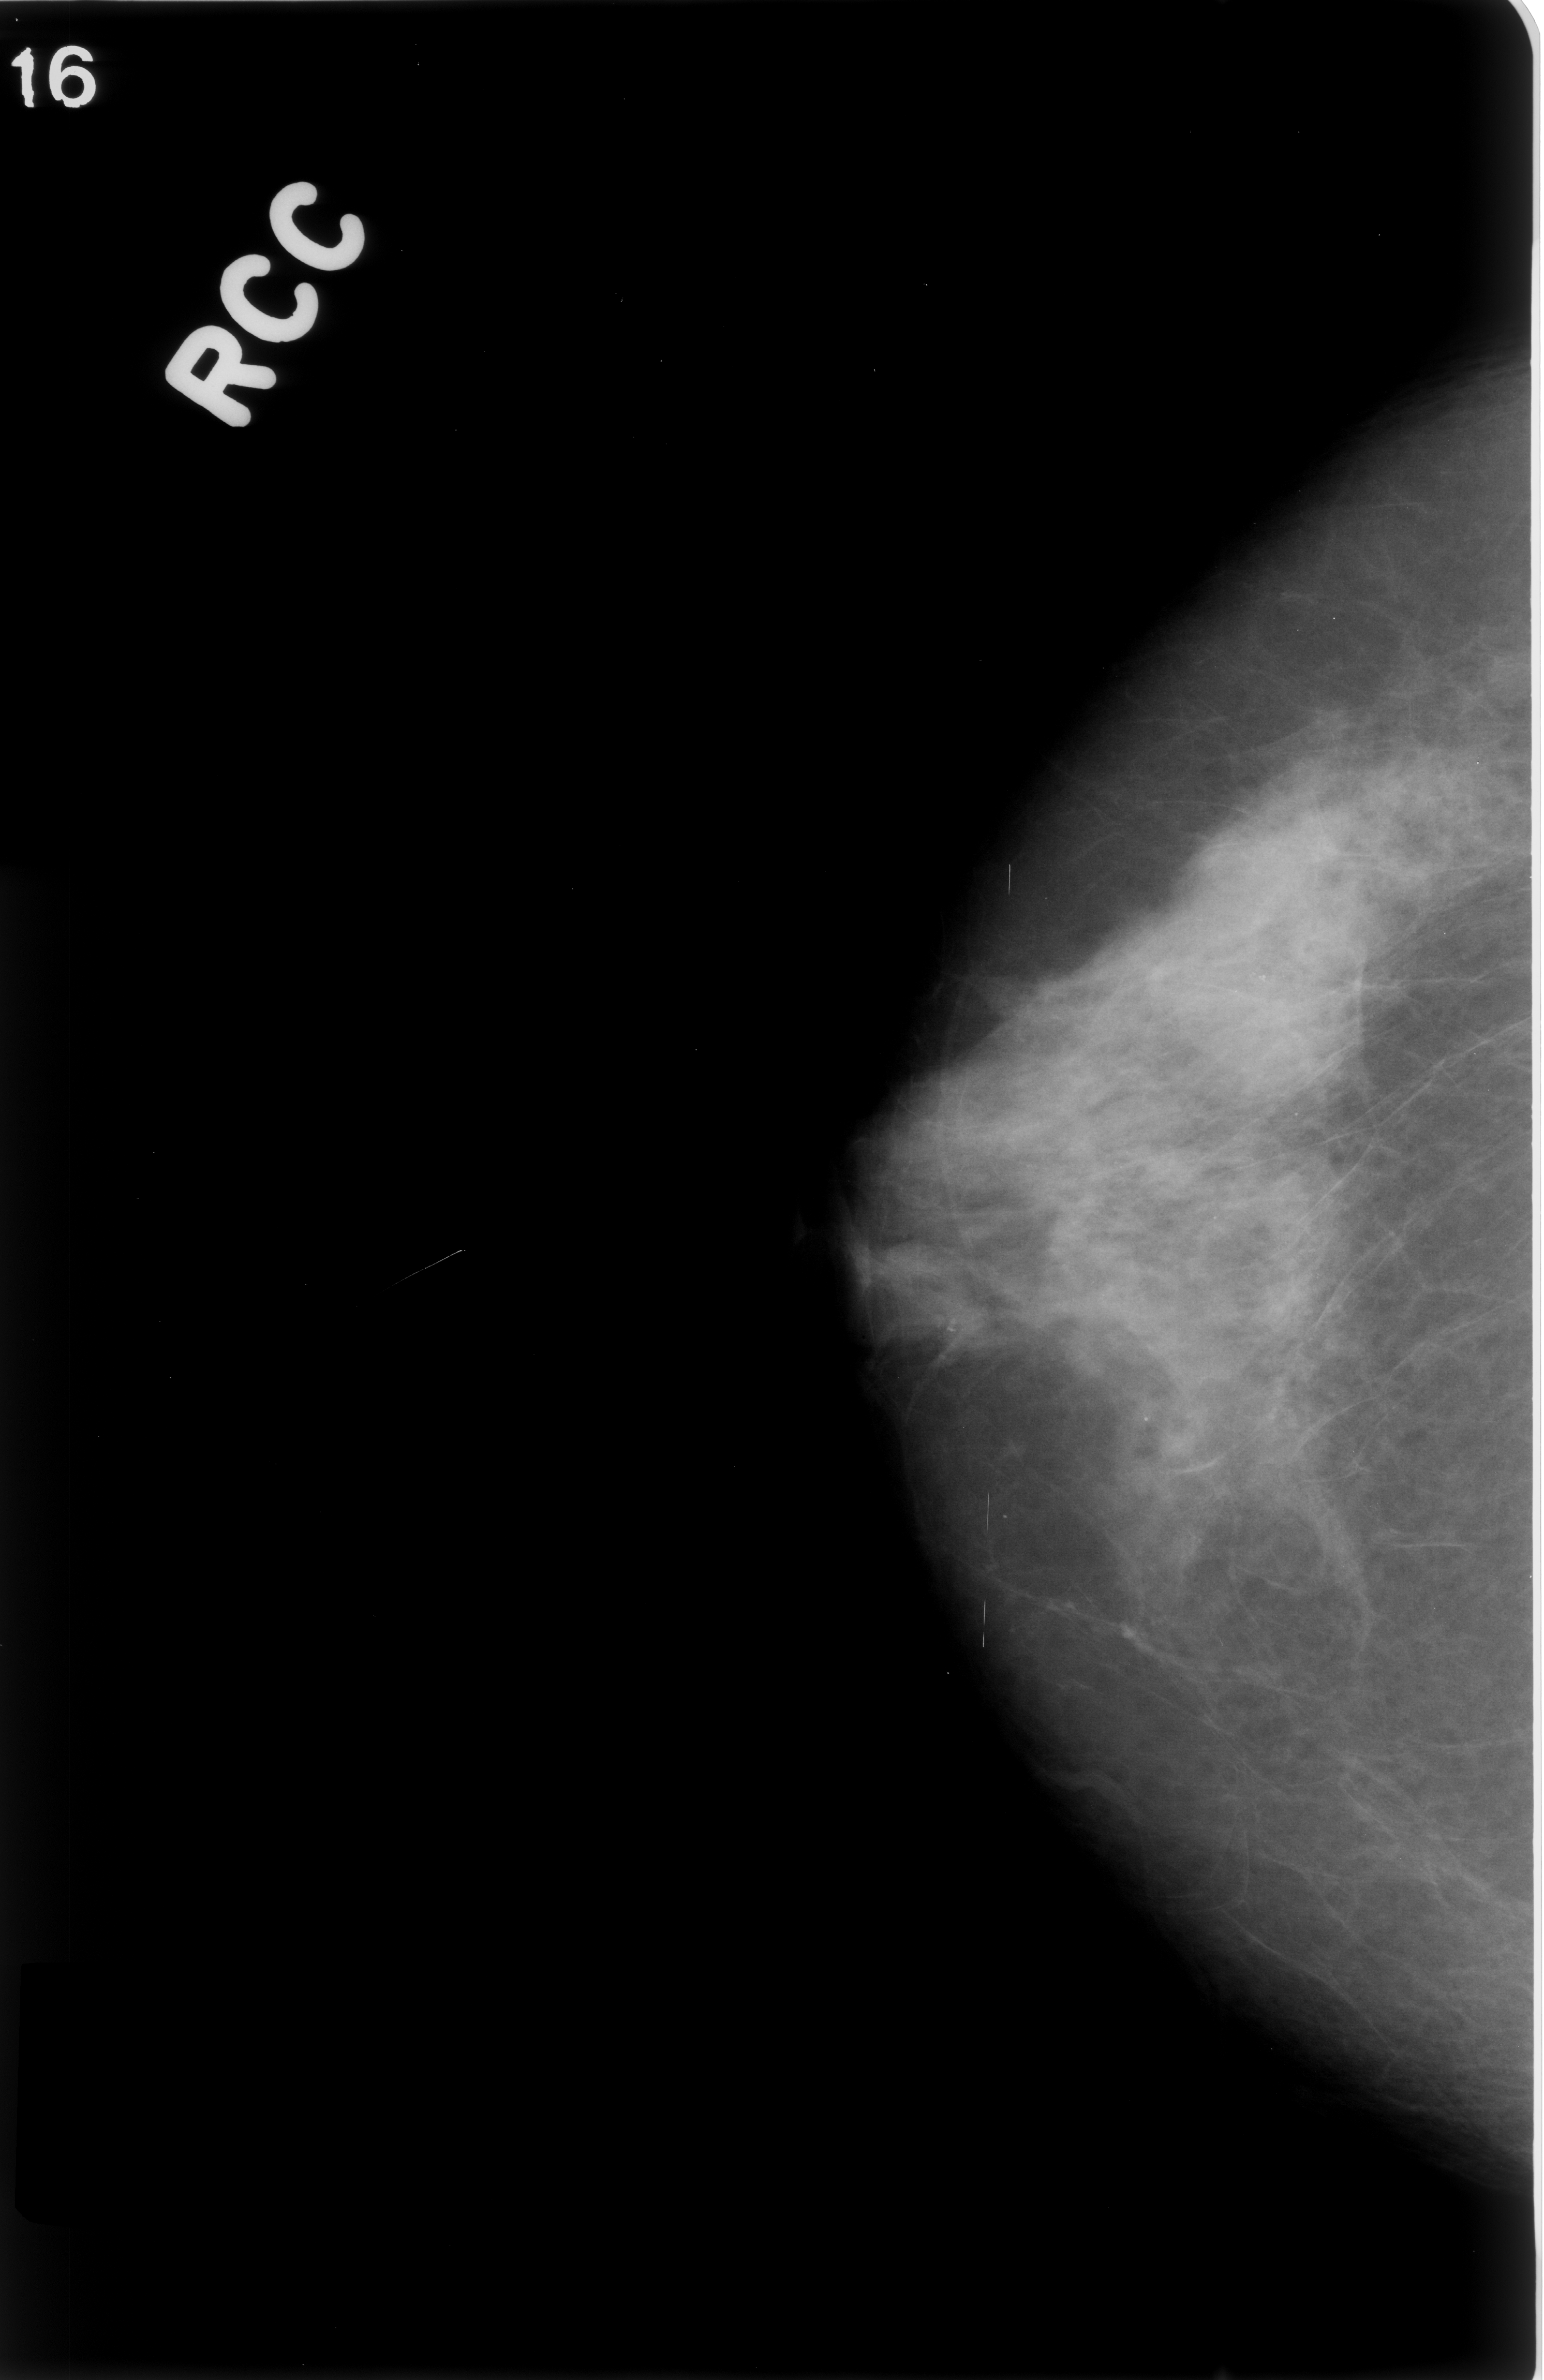
Scanned film-screen mammogram. Right breast. CC view. 1544 × 2380 image matrix.
Expert-marked regions of interest on this image (one box per marked abnormality):
- Finding 1 of 2: calcifications, morphology amorphous, distribution clustered; BI-RADS assessment category 4; pathology result (as recorded, not read from the image): benign: bounding box [x1, y1, x2, y2] px = [873, 1262, 1015, 1400]
- Finding 2 of 2: calcifications, morphology amorphous, distribution clustered; BI-RADS assessment category 4; subtlety rating 3 on a 1 (subtle) to 5 (obvious) scale; pathology result (as recorded, not read from the image): malignant: [1142, 873, 1350, 1056]